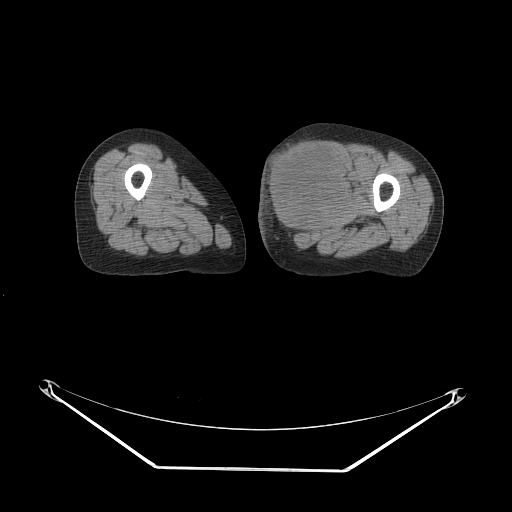
CT of an extremity soft-tissue mass (from a PET/CT study), one axial slice. Slice 36 of 91 in the series (ordered by position). Reconstruction kernel STANDARD. 140 kVp. Soft-tissue window (W 400 / L 40 HU). 512 × 512 image matrix. Female patient. From the clinical record (not read from this slice): histological type: pleomorphic leiomyosarcoma; grade: high; site of the primary tumour: left thigh.
Annotated regions visible in this slice (expert contour drawn on MRI and transferred to this co-registered scan by the dataset authors):
- gross tumour volume including surrounding oedema: box from (x=263, y=137) to (x=355, y=236) px
- gross tumour volume (mass): (x=263, y=137)–(x=350, y=234)